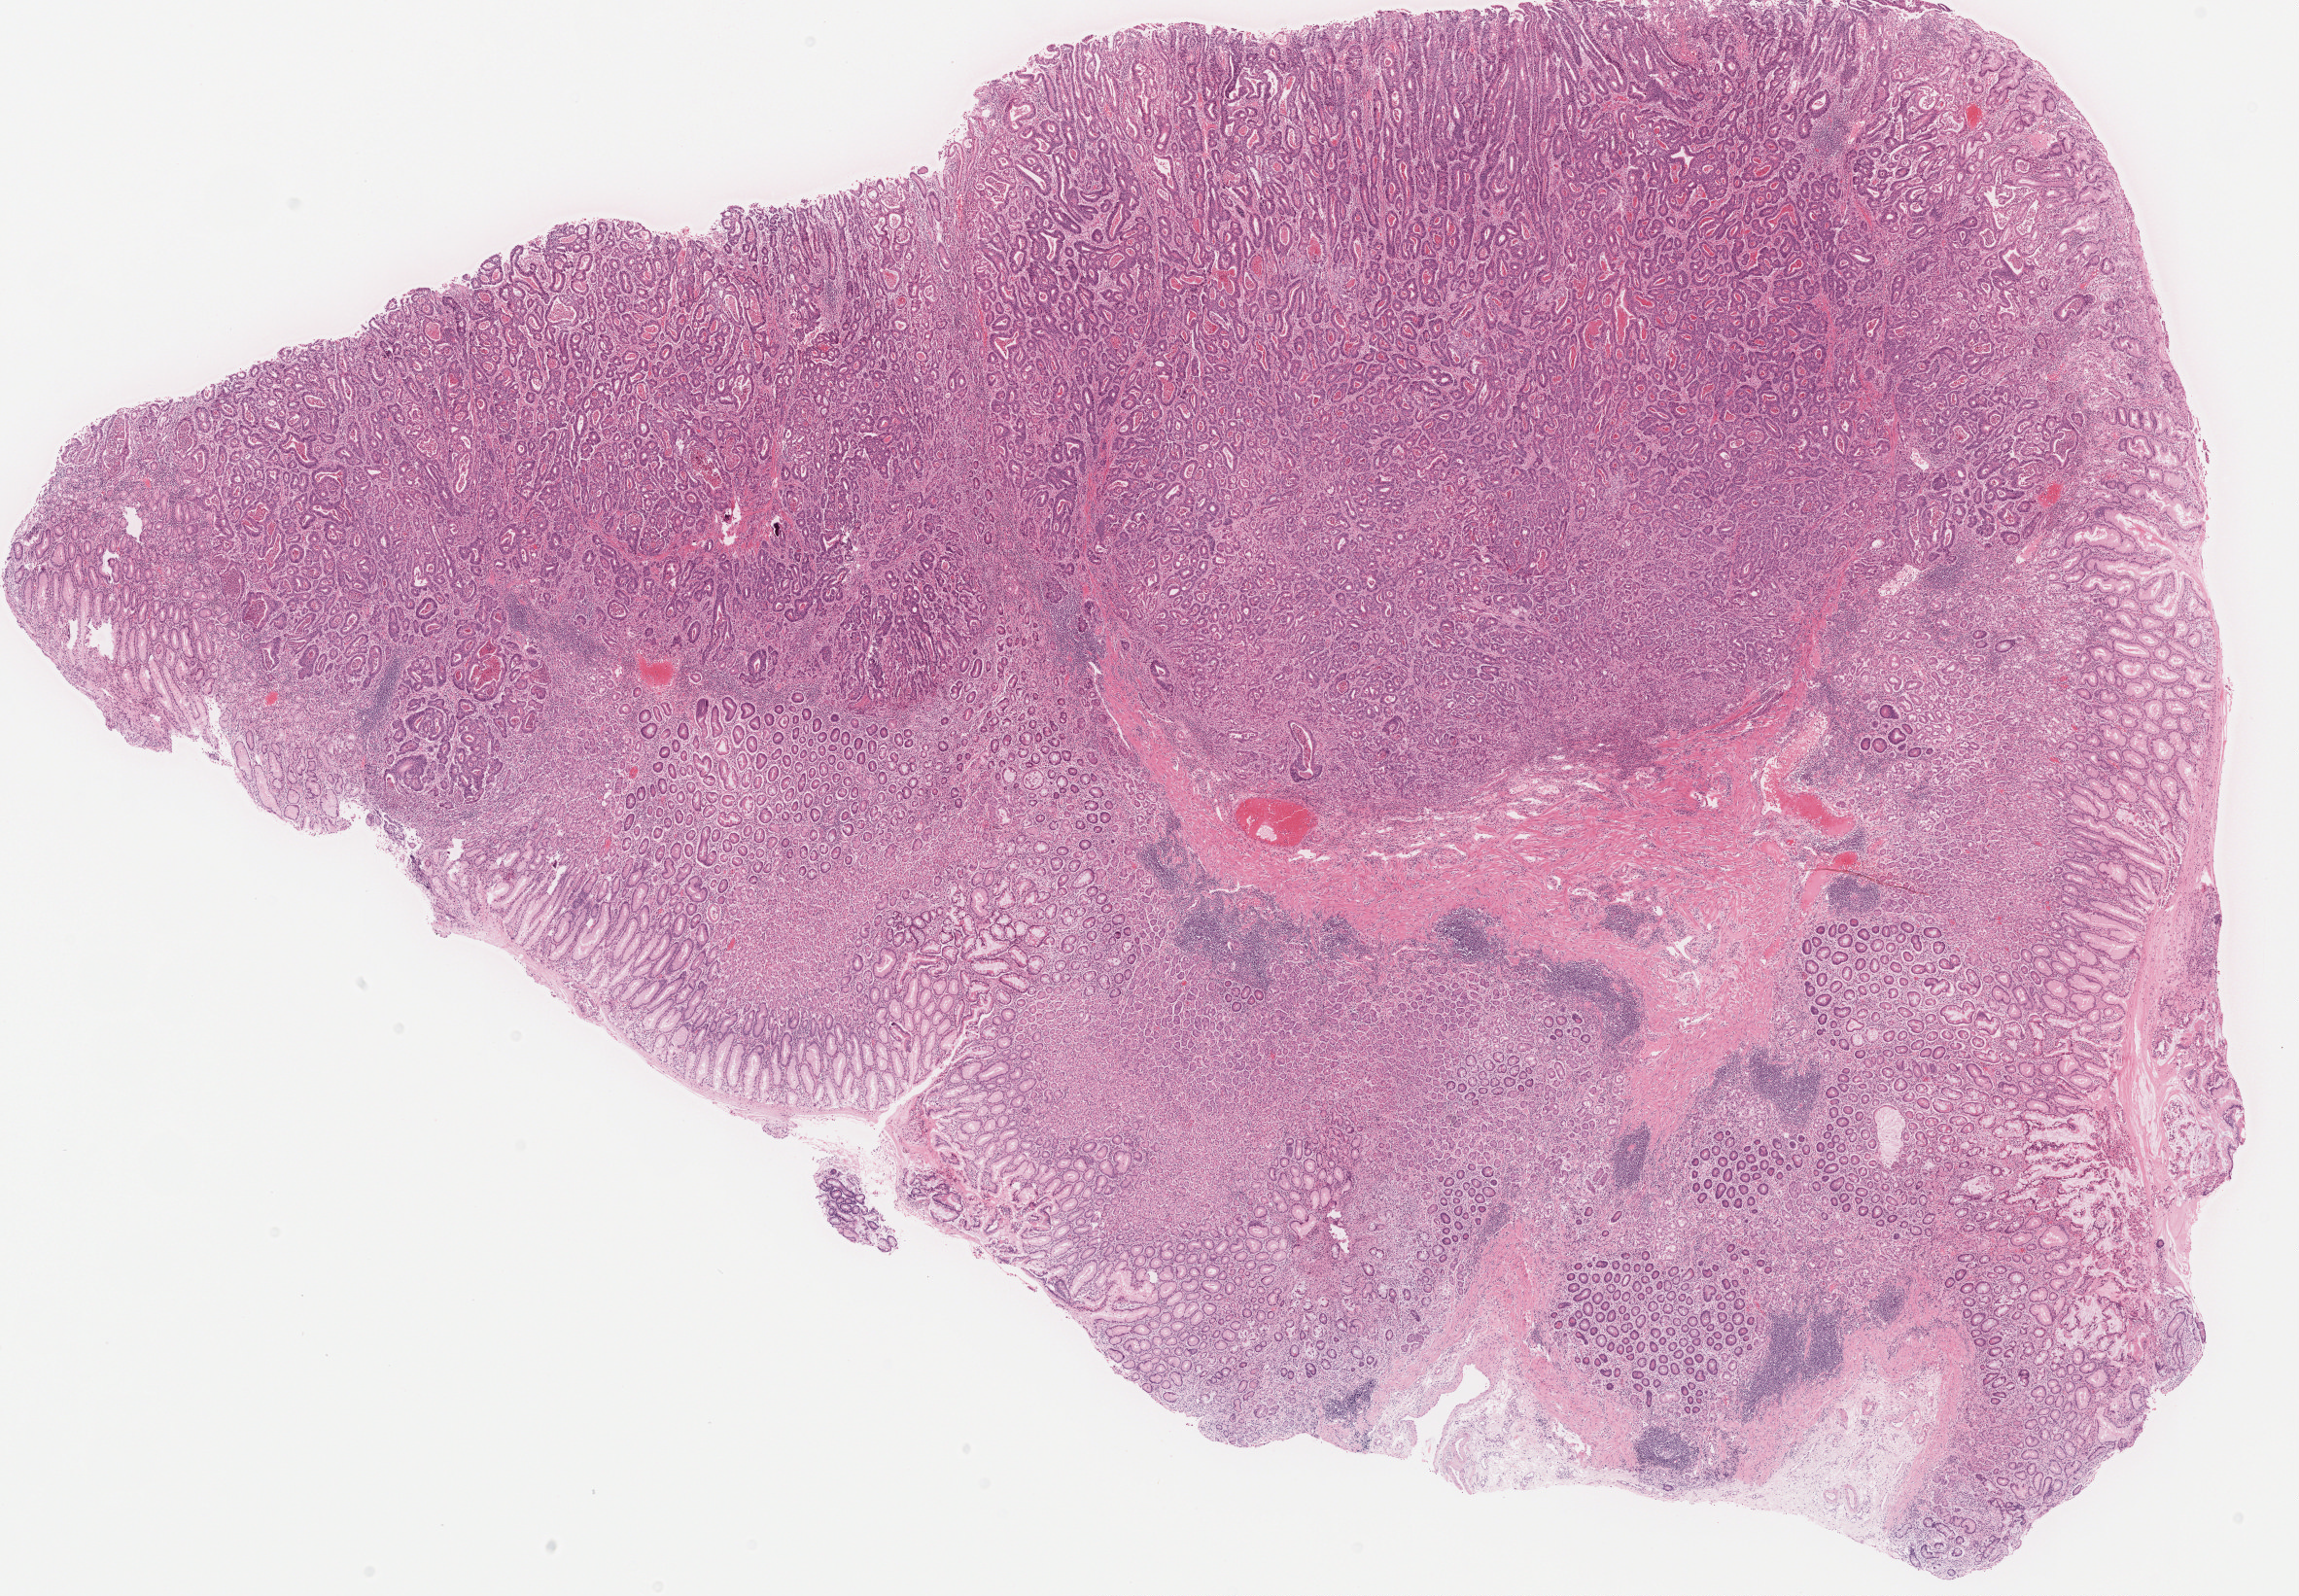
H&E-stained whole-slide image — a low-resolution overview of the entire scanned area, about 18.7 x 13.0 mm (acquisition: 20x scan), formalin-fixed paraffin-embedded (FFPE) diagnostic section, primary tumour sample from the stomach. Male patient; age at initial diagnosis 71 years.
Pathologic diagnosis: Tubular adenocarcinoma (gastric antrum).